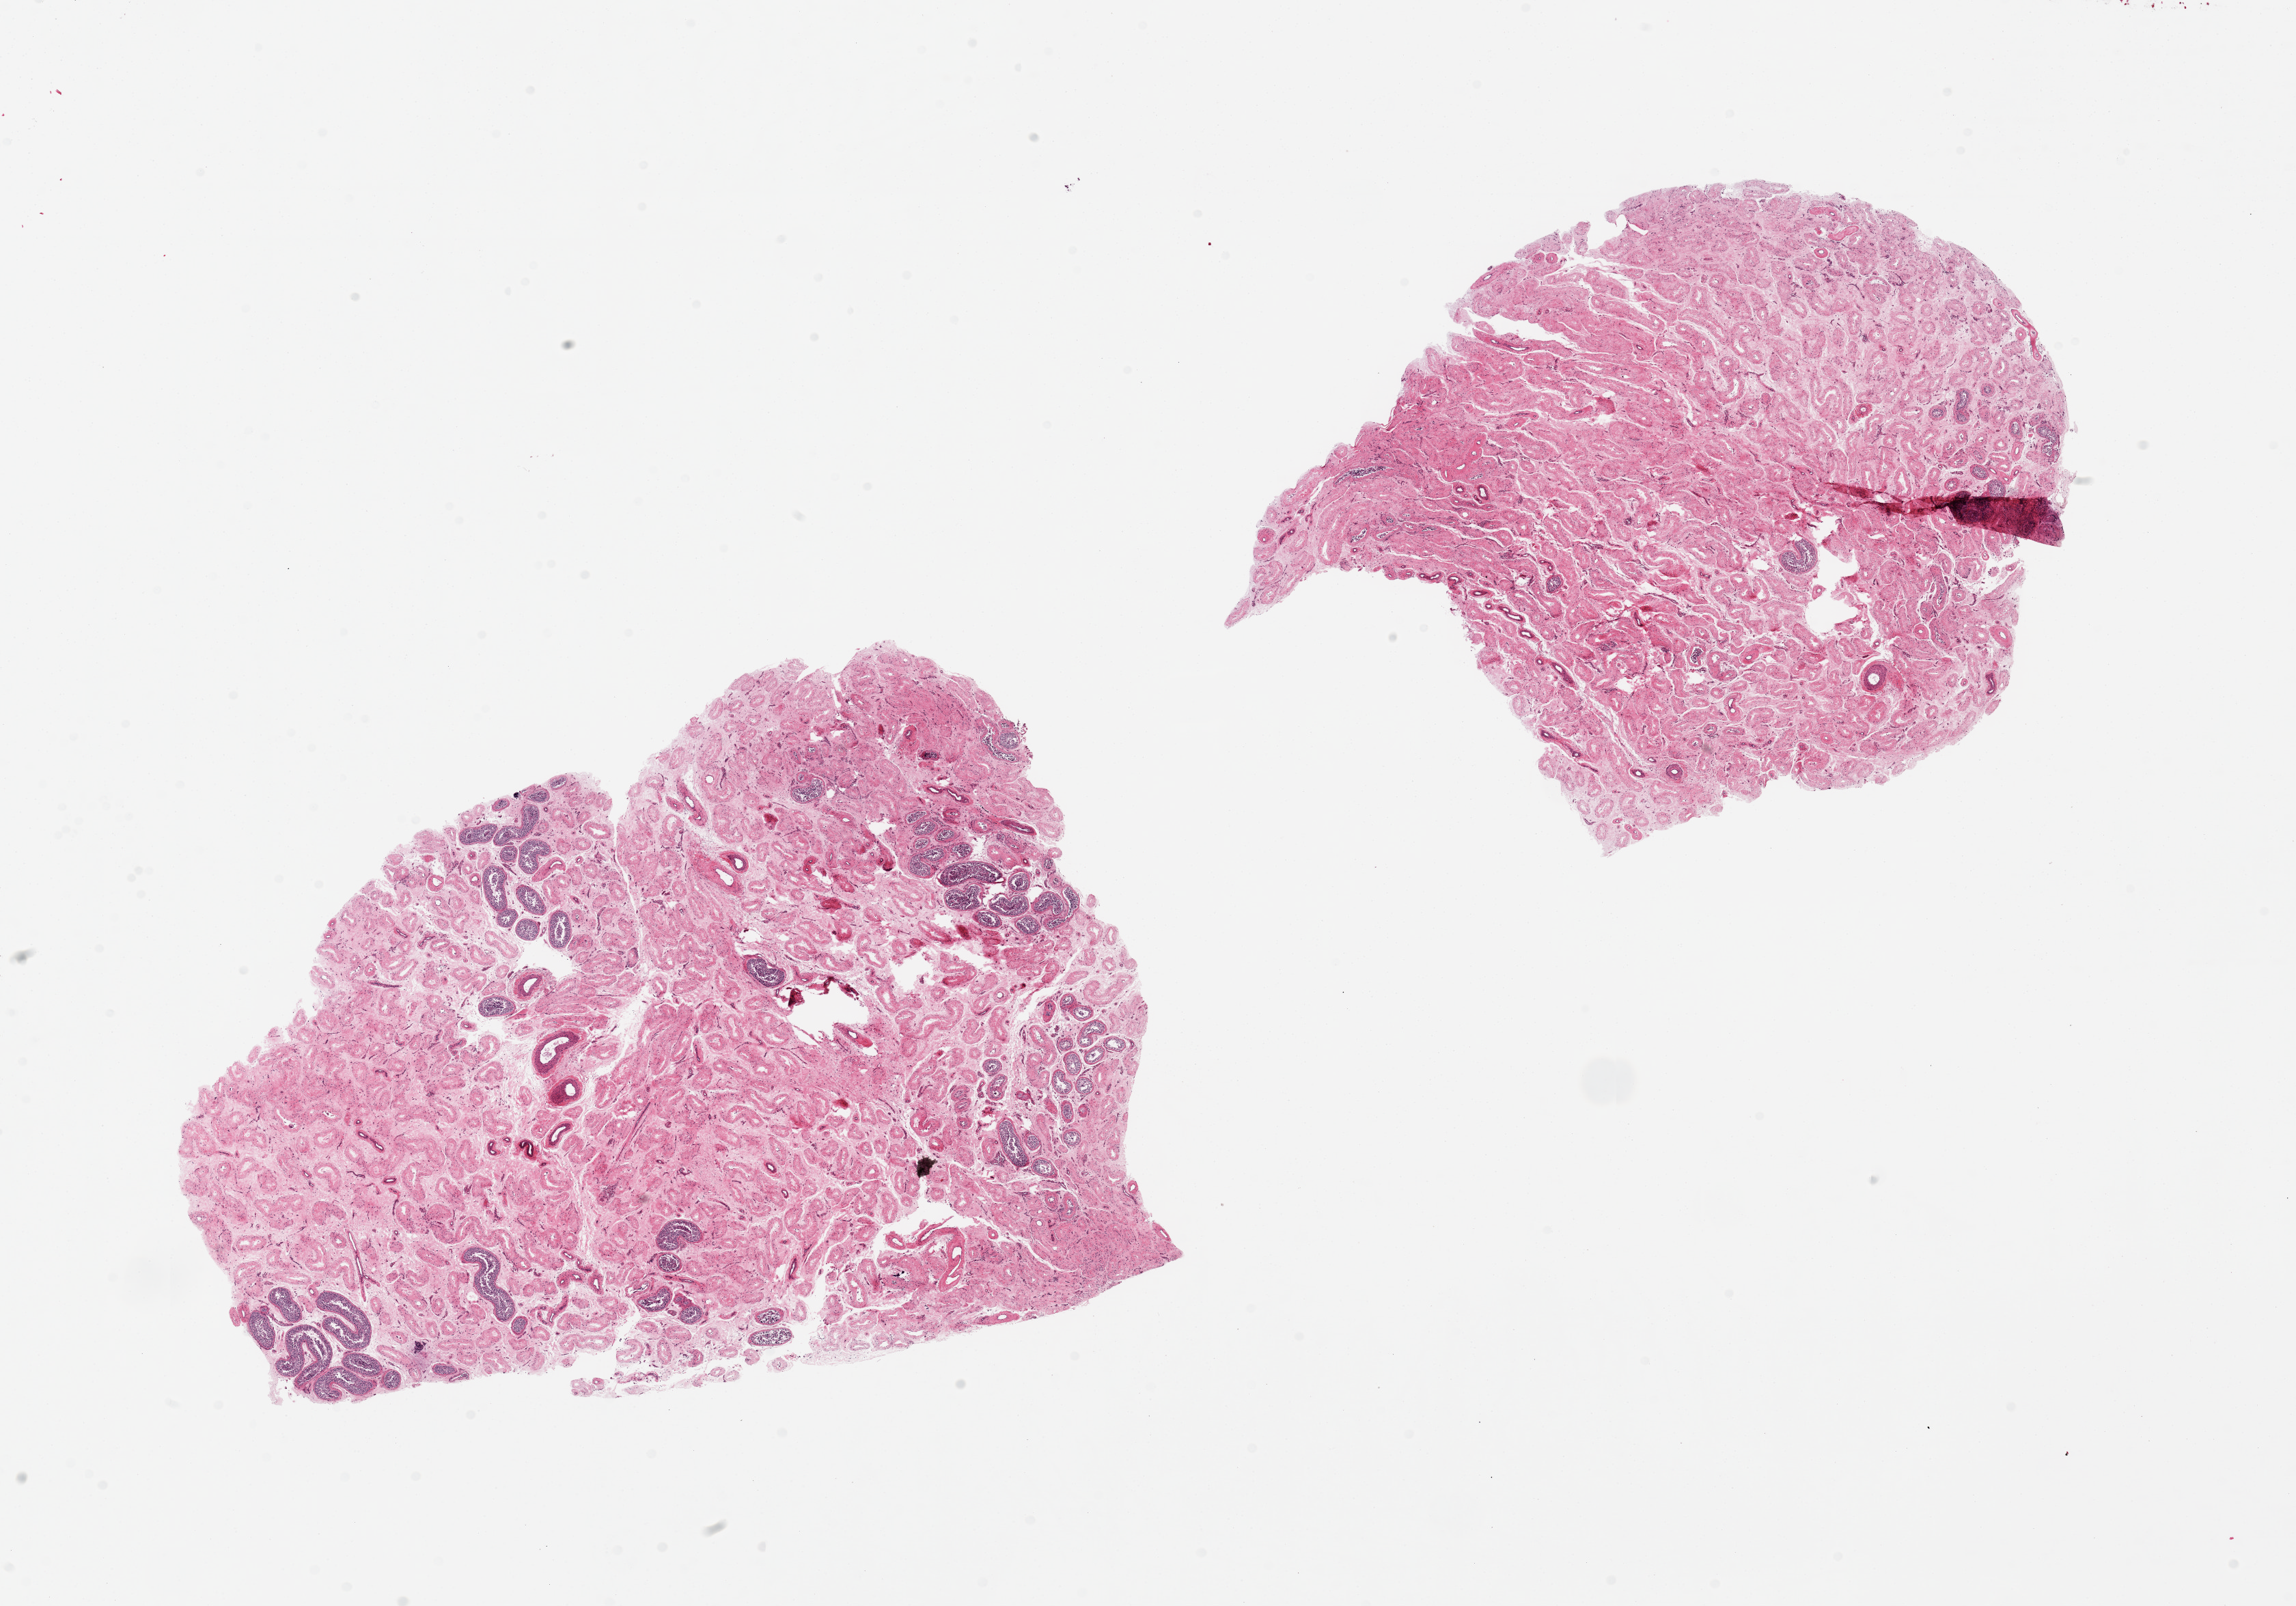
Haematoxylin and eosin whole-slide image, brightfield, shown as a low-resolution overview of the whole scanned area (about 26.6 x 18.6 mm), PAXgene-fixed, paraffin-embedded tissue, target tissue: testis, donor tissue sample. Male donor.
Reviewer comment on this tissue sample: 2 pieces, 11x8 & 10x7.5mm; generalized tubular atrophy, empty lumina; ~1% of tubules with spermatogenesis.